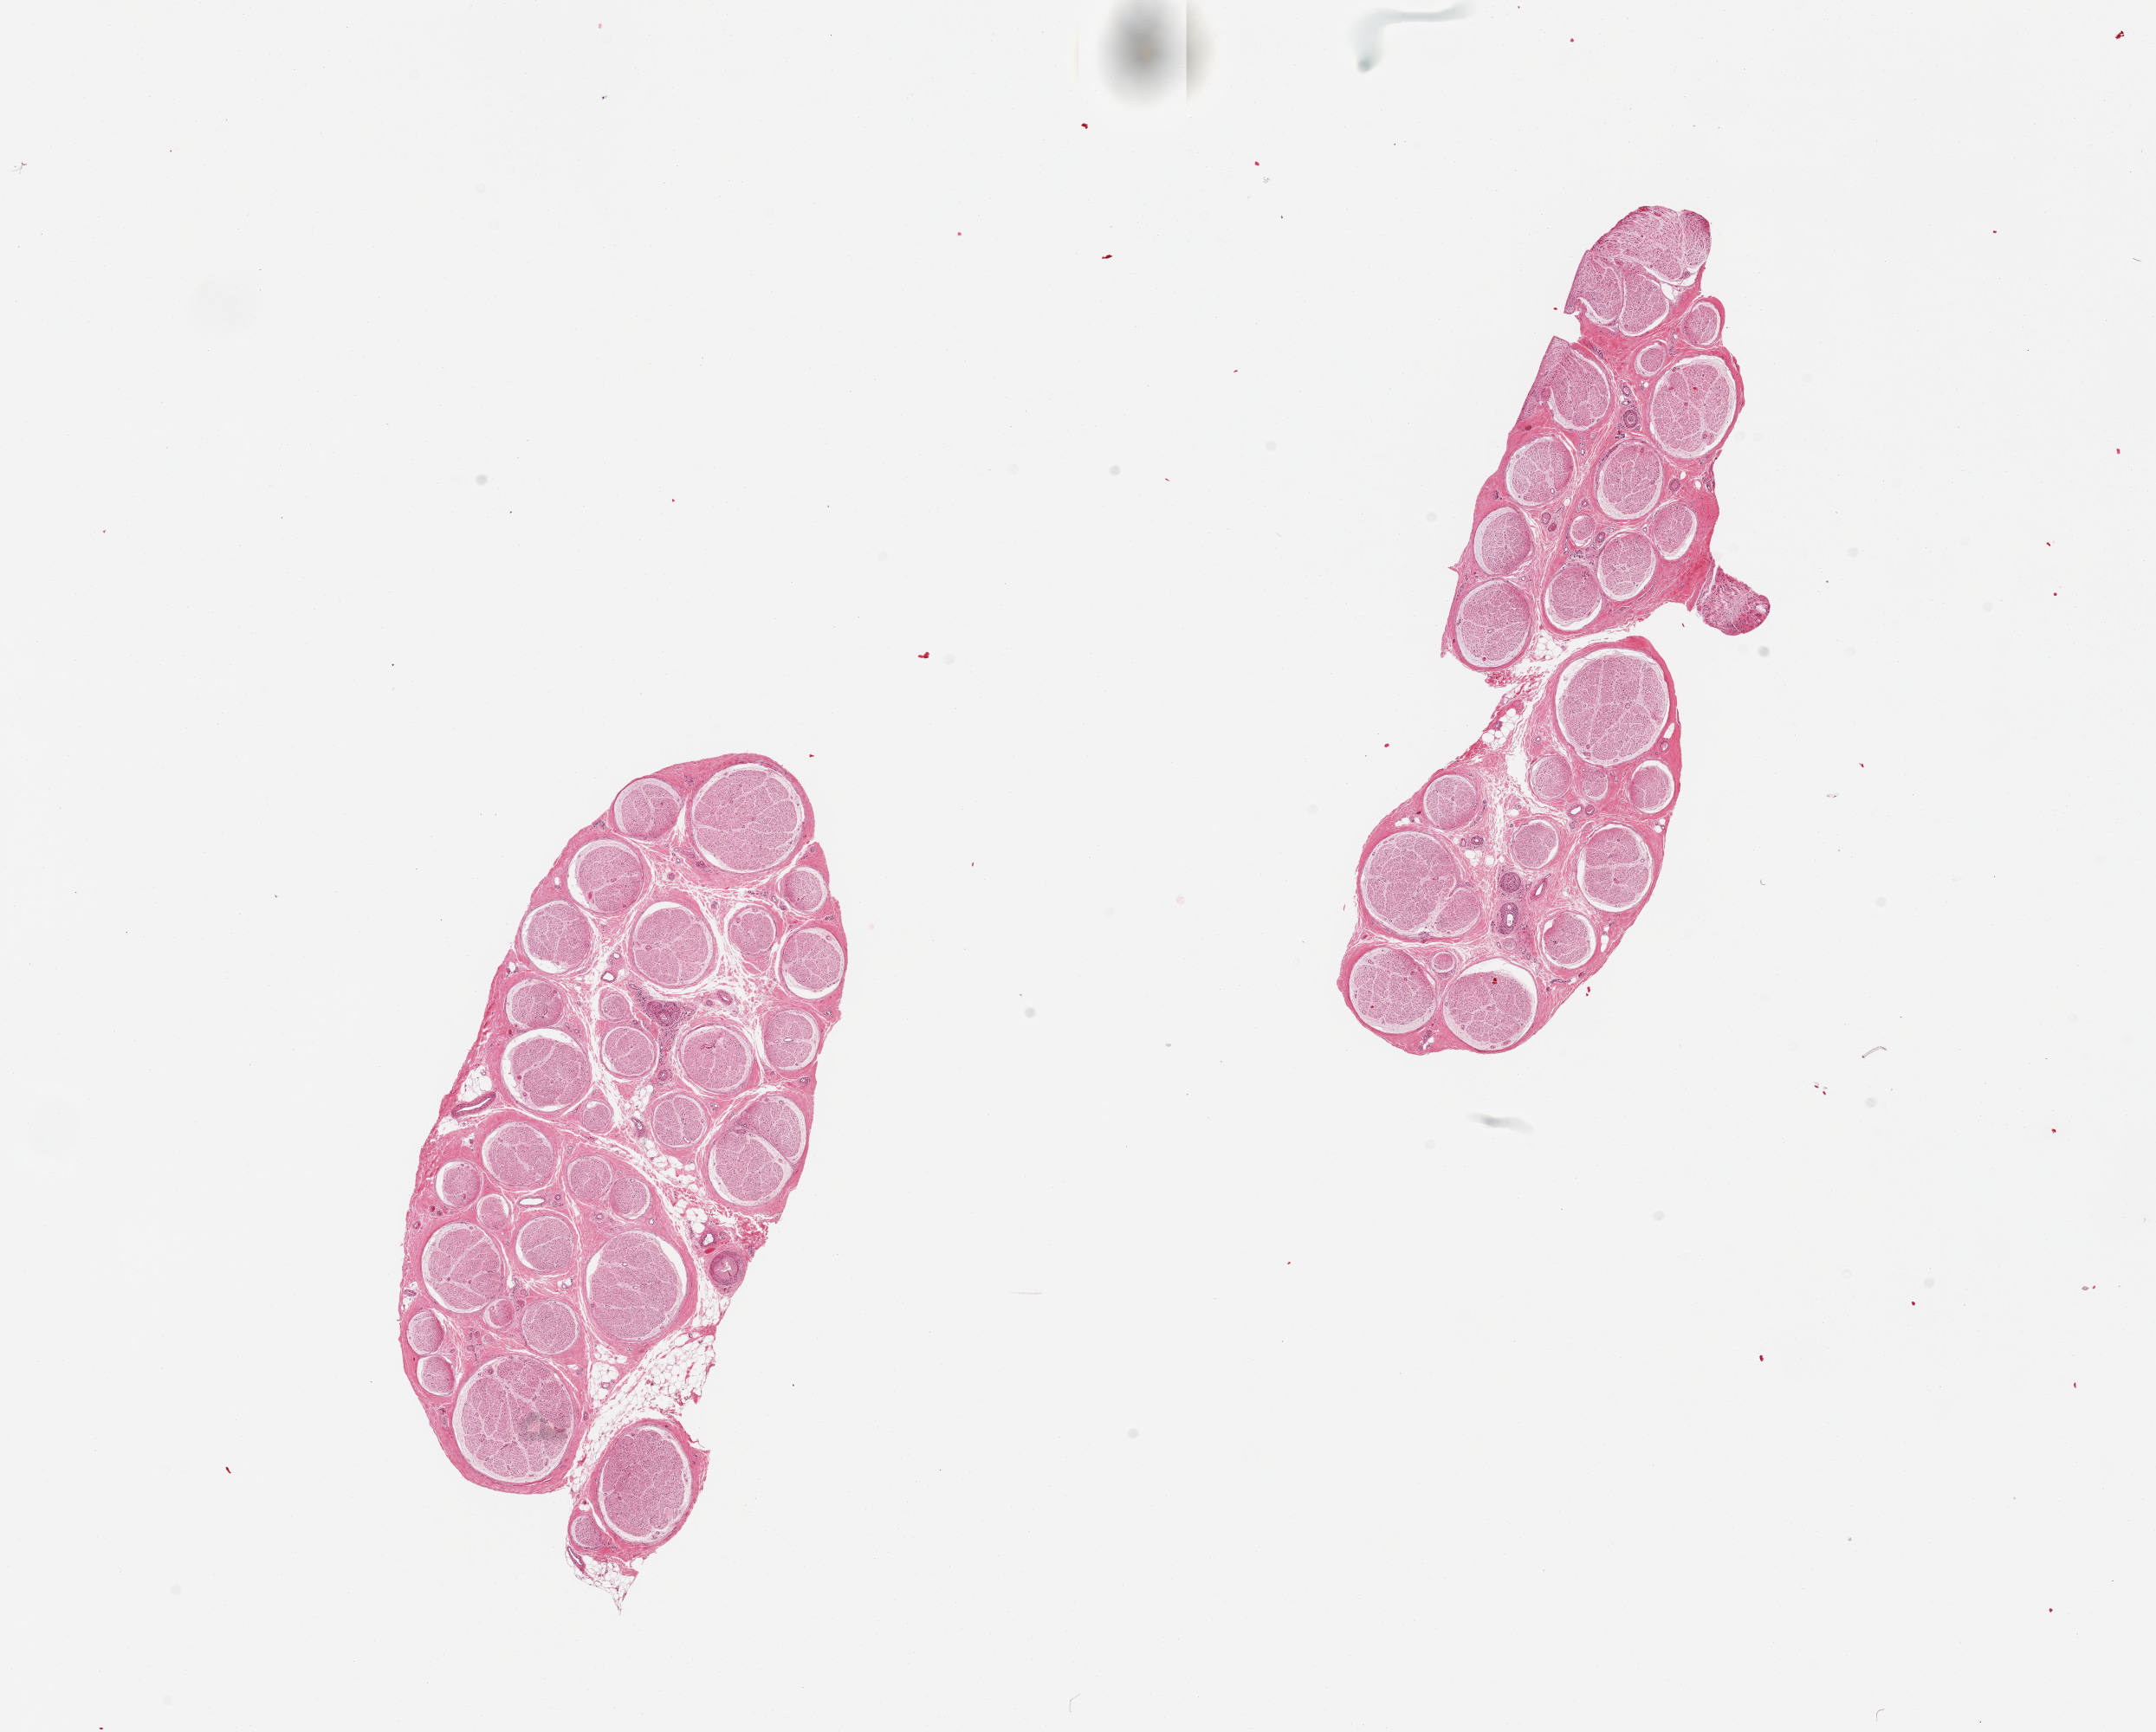
H&E whole-slide image, whole scanned area (about 19.7 x 15.8 mm) shown as a low-resolution overview; PAXgene-fixed, paraffin-embedded tissue; target tissue: tibial nerve; donor tissue sample. Donor: male.
- pathologist's review note for this sample: 2 pieces, no adherent fat, clean specimens